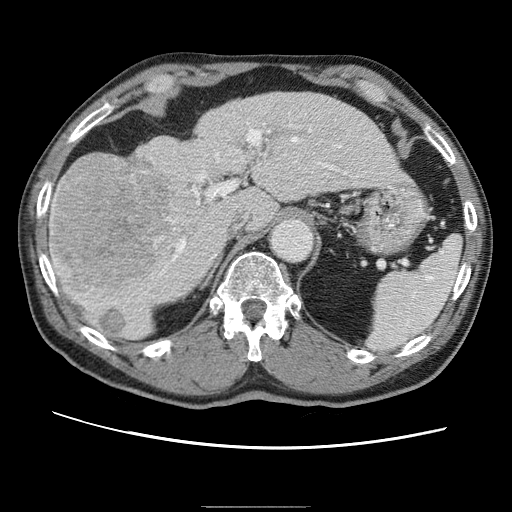
Contrast-enhanced abdominal CT (liver protocol), one axial slice. Position 37 of 75 along the scan axis. Reconstruction kernel STANDARD. One of 2 acquisitions stored at this slice position. Soft-tissue window (W 400 / L 40 HU). 2.5 mm slice thickness. 512 × 512 image matrix. From the clinical record (not read from this slice): diagnosis: hepatocellular carcinoma (patient treated with transarterial chemoembolisation; whether this scan precedes or follows treatment is not stated here); TNM stage (as recorded): Stage-II; Child-Pugh class: A; tumour differentiation: well differentiated; tumour nodularity: multinodular.
Structures marked on this image (semi-automatically segmented with operator editing):
- liver parenchyma outside the tumour (the mass and vessels are separate outlines, so this box may not span the whole liver): bounding box (x1, y1, x2, y2) in pixels: (50, 94, 398, 338)
- mass: (49, 158, 170, 308)
- liver vessels: (136, 126, 317, 303)